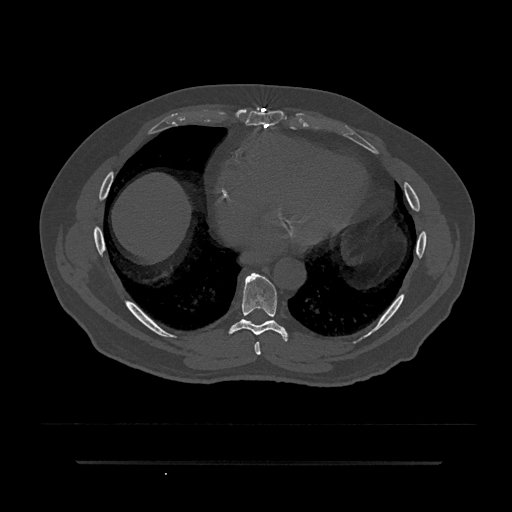
CT including the spine, one axial slice; position 429 of 797 along the scan axis; reconstruction kernel Br40s/3; bone window (W 1800 / L 400 HU); 0.5 mm slice thickness; 512 × 512 image matrix, field of view 464 × 464 mm. Patient: male, 59 years. From the clinical record (not read from this slice): primary cancer: bile ducts; vertebrae with lytic lesions (as recorded): T10.
Structures marked on this image (semi-automatically segmented with operator editing):
- T7 vertebra: box from (x=254, y=342) to (x=261, y=355) px
- T8 vertebra: (x=229, y=273)–(x=288, y=342)